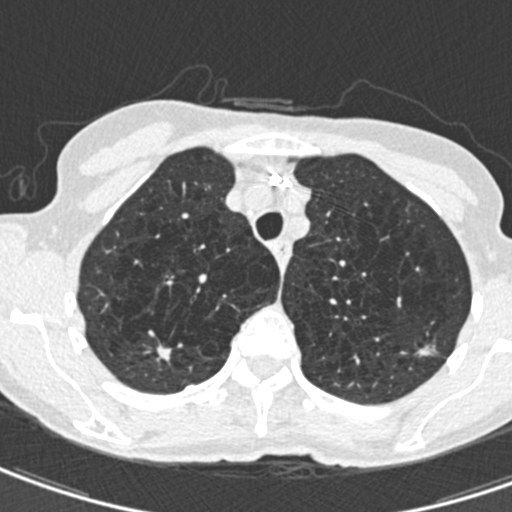
Chest CT (low-dose screening protocol), one axial image, second annual screen, lung window (W 1500 / L -600 HU), 0.75 mm slice thickness, standard (soft-tissue) reconstruction kernel (B30f), slice 113 of 498 in the series, 512 × 512 image matrix, field of view 272 × 272 mm. Female participant, aged 71 years at enrolment. Current smoker at enrolment.
Lesion marked by an expert reader, bounding box (x1, y1, x2, y2) in pixels: (405, 332, 445, 370). The screening reader recorded 2 non-calcified nodules or masses ≥4 mm on this exam; which of them this box marks is not recorded. Later outcome: lung cancer diagnosed 604 days after this screen — adenocarcinoma, NOS, left upper lobe, moderately differentiated (G2), stage IA (AJCC 6th edition), 12 mm at pathology.